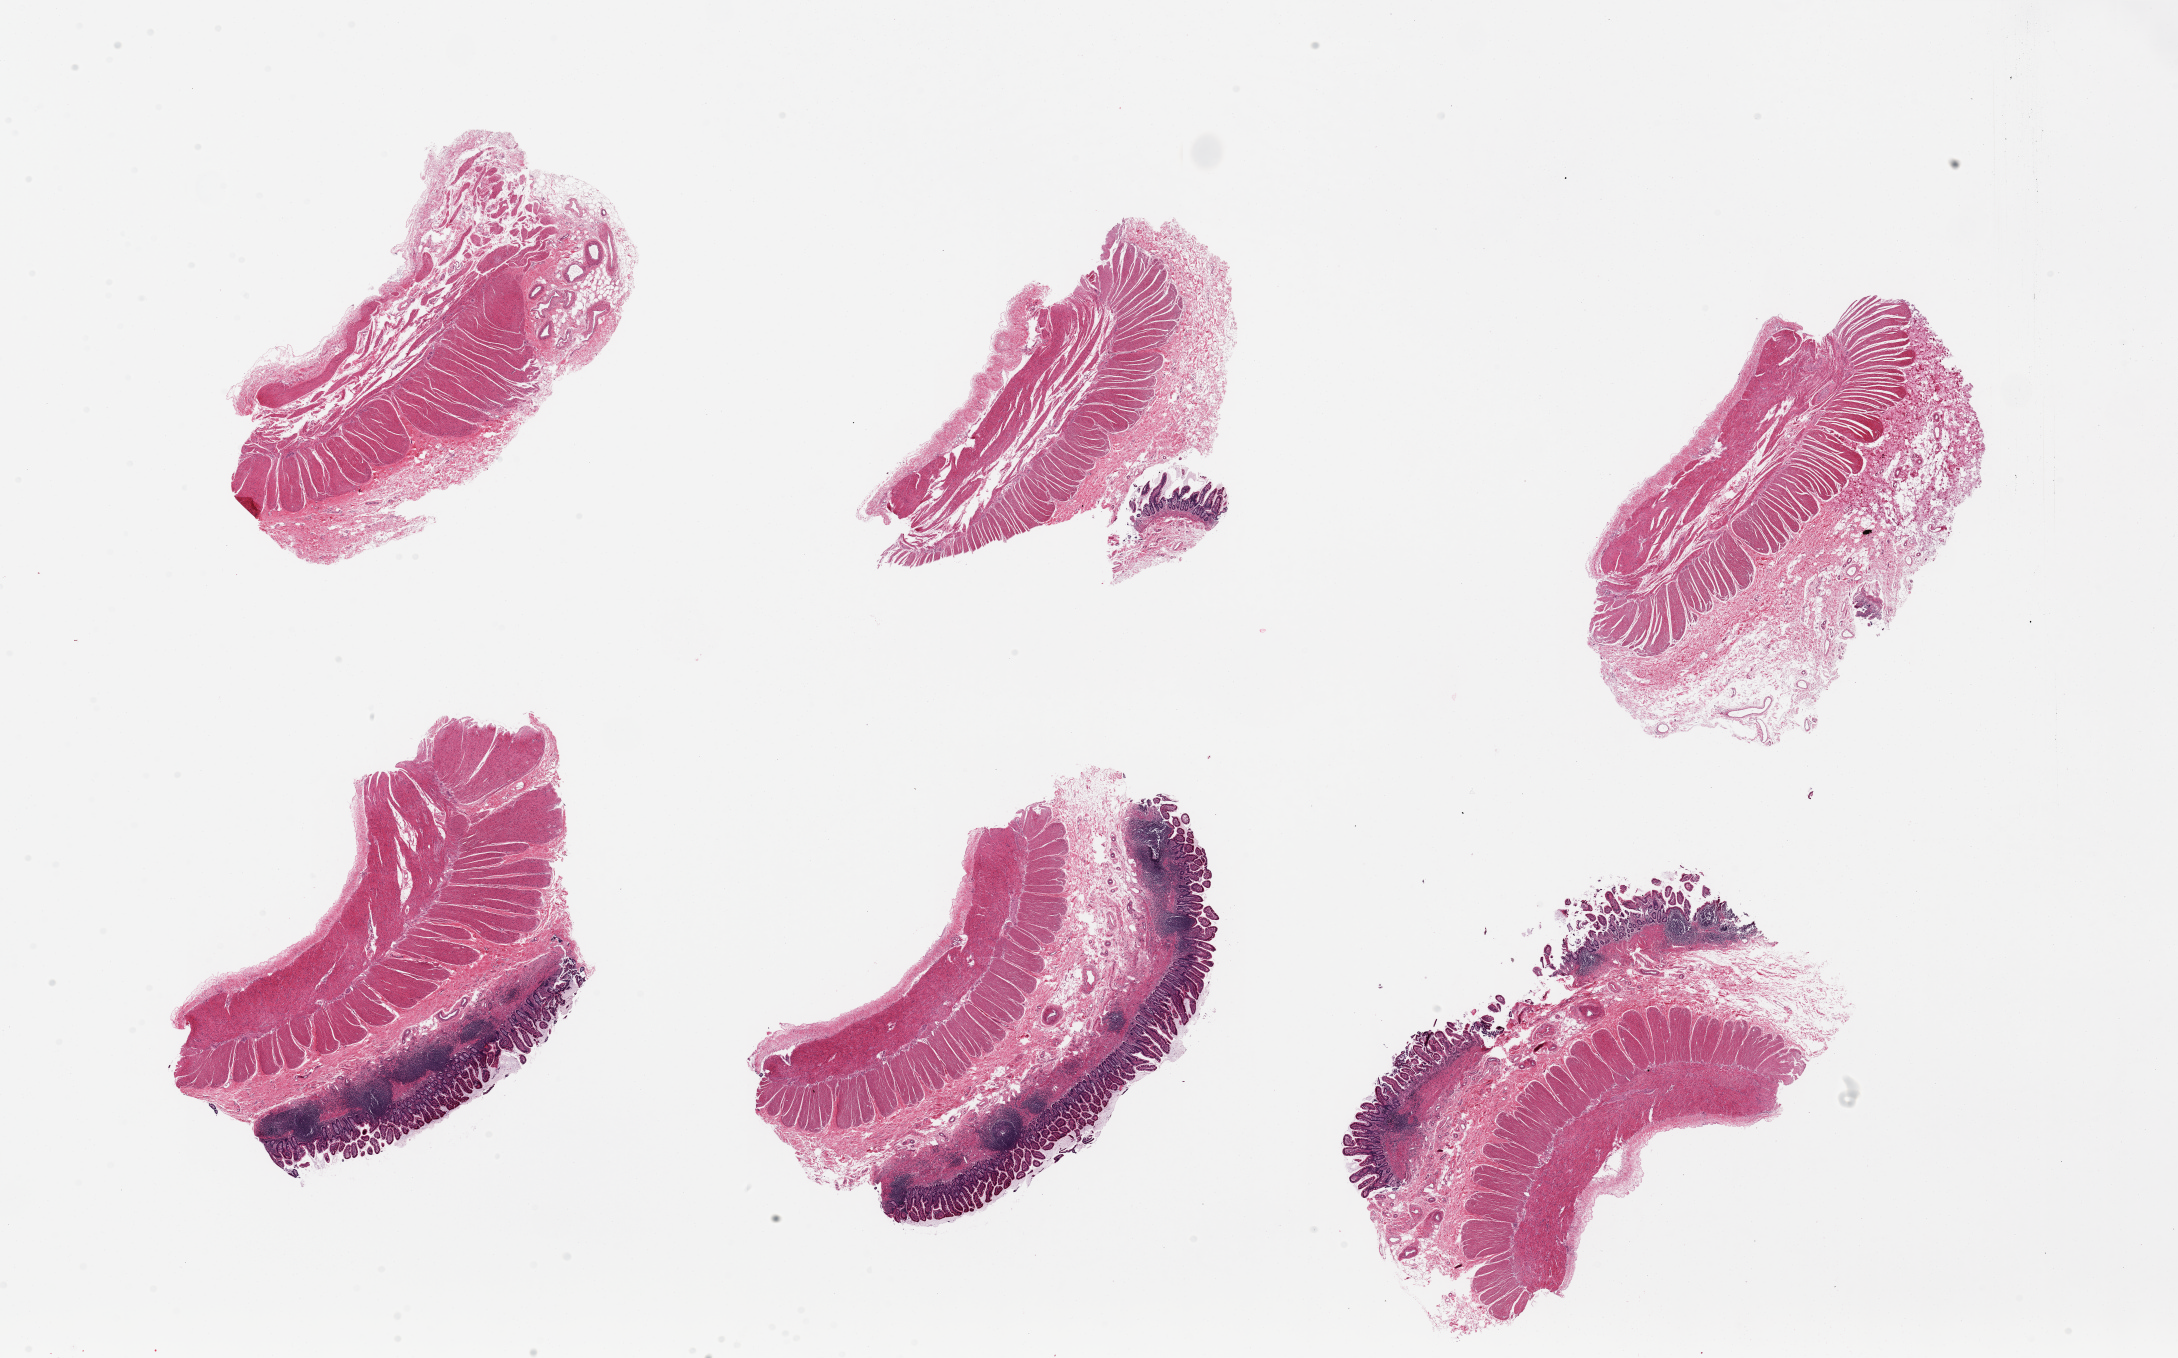
Haematoxylin and eosin whole-slide image — shown as a low-resolution overview of the whole scanned area (about 34.5 x 21.5 mm, acquisition: 20x scan); PAXgene-fixed, paraffin-embedded tissue; section of ileum (target tissue); tissue donor sample. Male donor.
- pathologist's review note for this sample: 6 pieces, up to 8x5mm; 3/6 with mucosa, well-preserved, lymphoid aggregates visible, ~10% total tissue